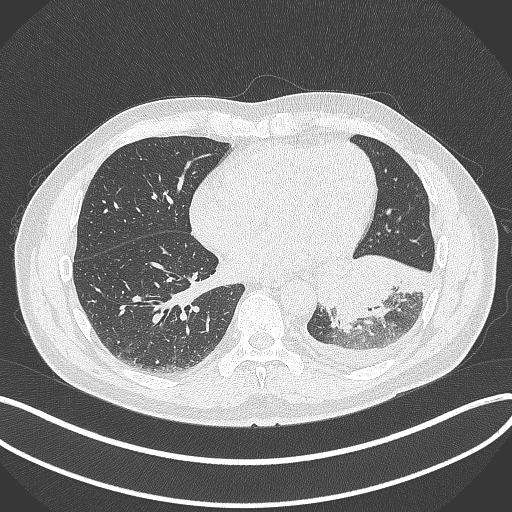
Chest CT, one axial slice; slice 131 of 342 in the series (ordered by position); lung window (W 1500 / L -600 HU); 1 mm slice thickness; 512 × 512 image matrix, field of view 400 × 400 mm. Male patient, age 58 years. From the clinical record (not read from this slice): clinical TNM (as recorded): T3 N1 M1b; histopathological grade: G3.
Structures marked on this image (bounding box drawn by a radiologist):
- lung tumour (recorded histology: small cell carcinoma): bounding box <314,246,432,337> (left, top, right, bottom; pixels)